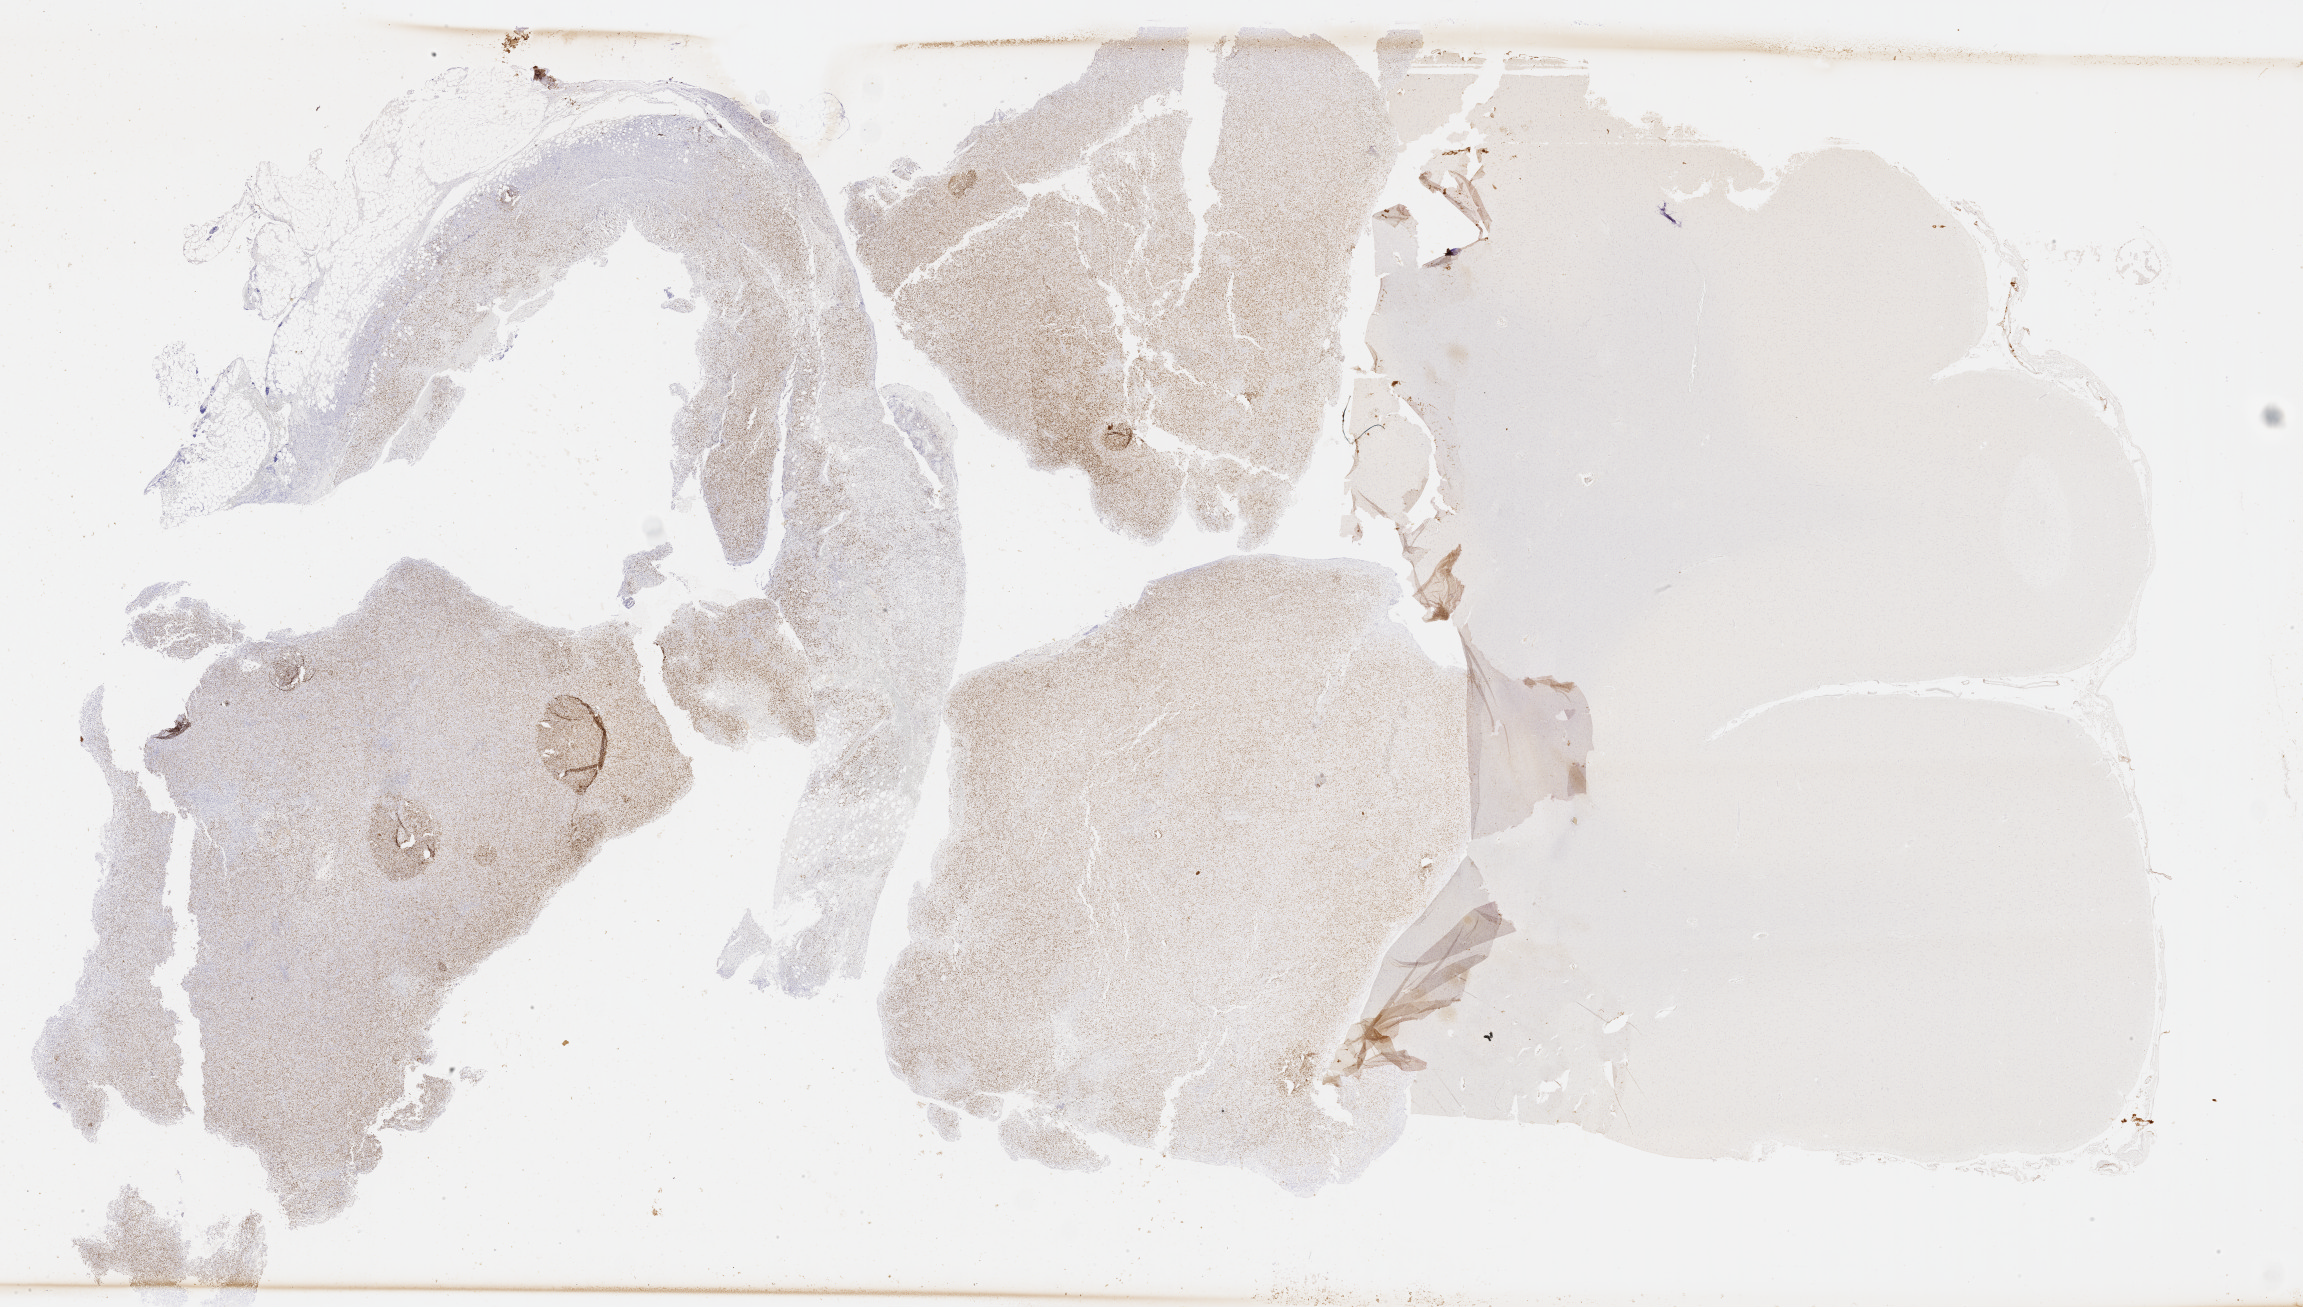
Whole-slide image, immunohistochemical stain for p53 — low-resolution overview of the scanned area, about 37.2 x 21.1 mm. Patient sex: female.
Specimen: tumor tissue.